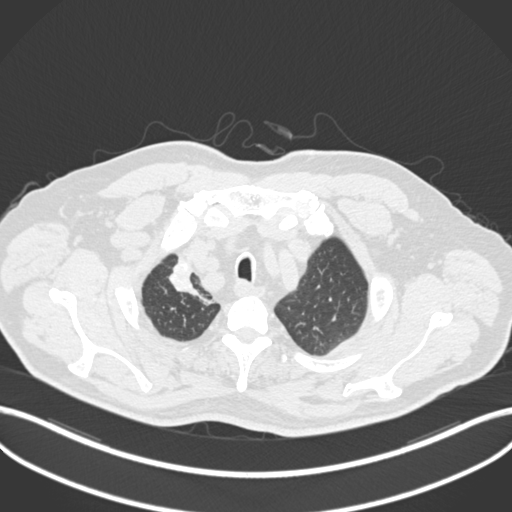
Chest CT, one axial slice; position 179 of 255 along the scan axis; reconstruction kernel B30f; 120 kVp; lung window (W 1500 / L -600 HU); 512 × 512 image matrix, field of view 400 × 400 mm. Male patient, age 60 years. From the clinical record (not read from this slice): clinical TNM (as recorded): T1b N1 M0.
Outlined on this slice (rectangle marked by the reading radiologist):
- lung tumour (recorded histology: squamous cell carcinoma): bounding box (x1, y1, x2, y2) in pixels: (163, 253, 213, 307)